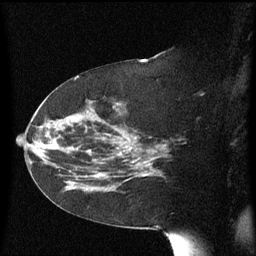
Breast MRI (dynamic contrast-enhanced), one sagittal slice; dynamic contrast-enhanced series, image 2 of 3 at this slice position (ordered by acquisition); 1.5 T; TE 4.2 ms, TR 8.4 ms; 2.3 mm slice thickness; 256 × 256 image matrix, field of view 200 × 200 mm. Patient: female, 63 years. Case-level facts recorded for this patient, not image findings: setting: breast cancer imaged before/during neoadjuvant chemotherapy; receptor status: HER2-positive.
Structures marked on this image (semi-automatic segmentation, software-assisted and operator-edited):
- analysis volume of interest (the breast-tissue region the enhancement analysis was run in; not a lesion): bounding box (x1, y1, x2, y2) in pixels: (63, 144, 147, 193)
- tumour enhancement mask (voxels above the 70 % enhancement threshold inside the analysis volume of interest): (97, 146, 146, 177)